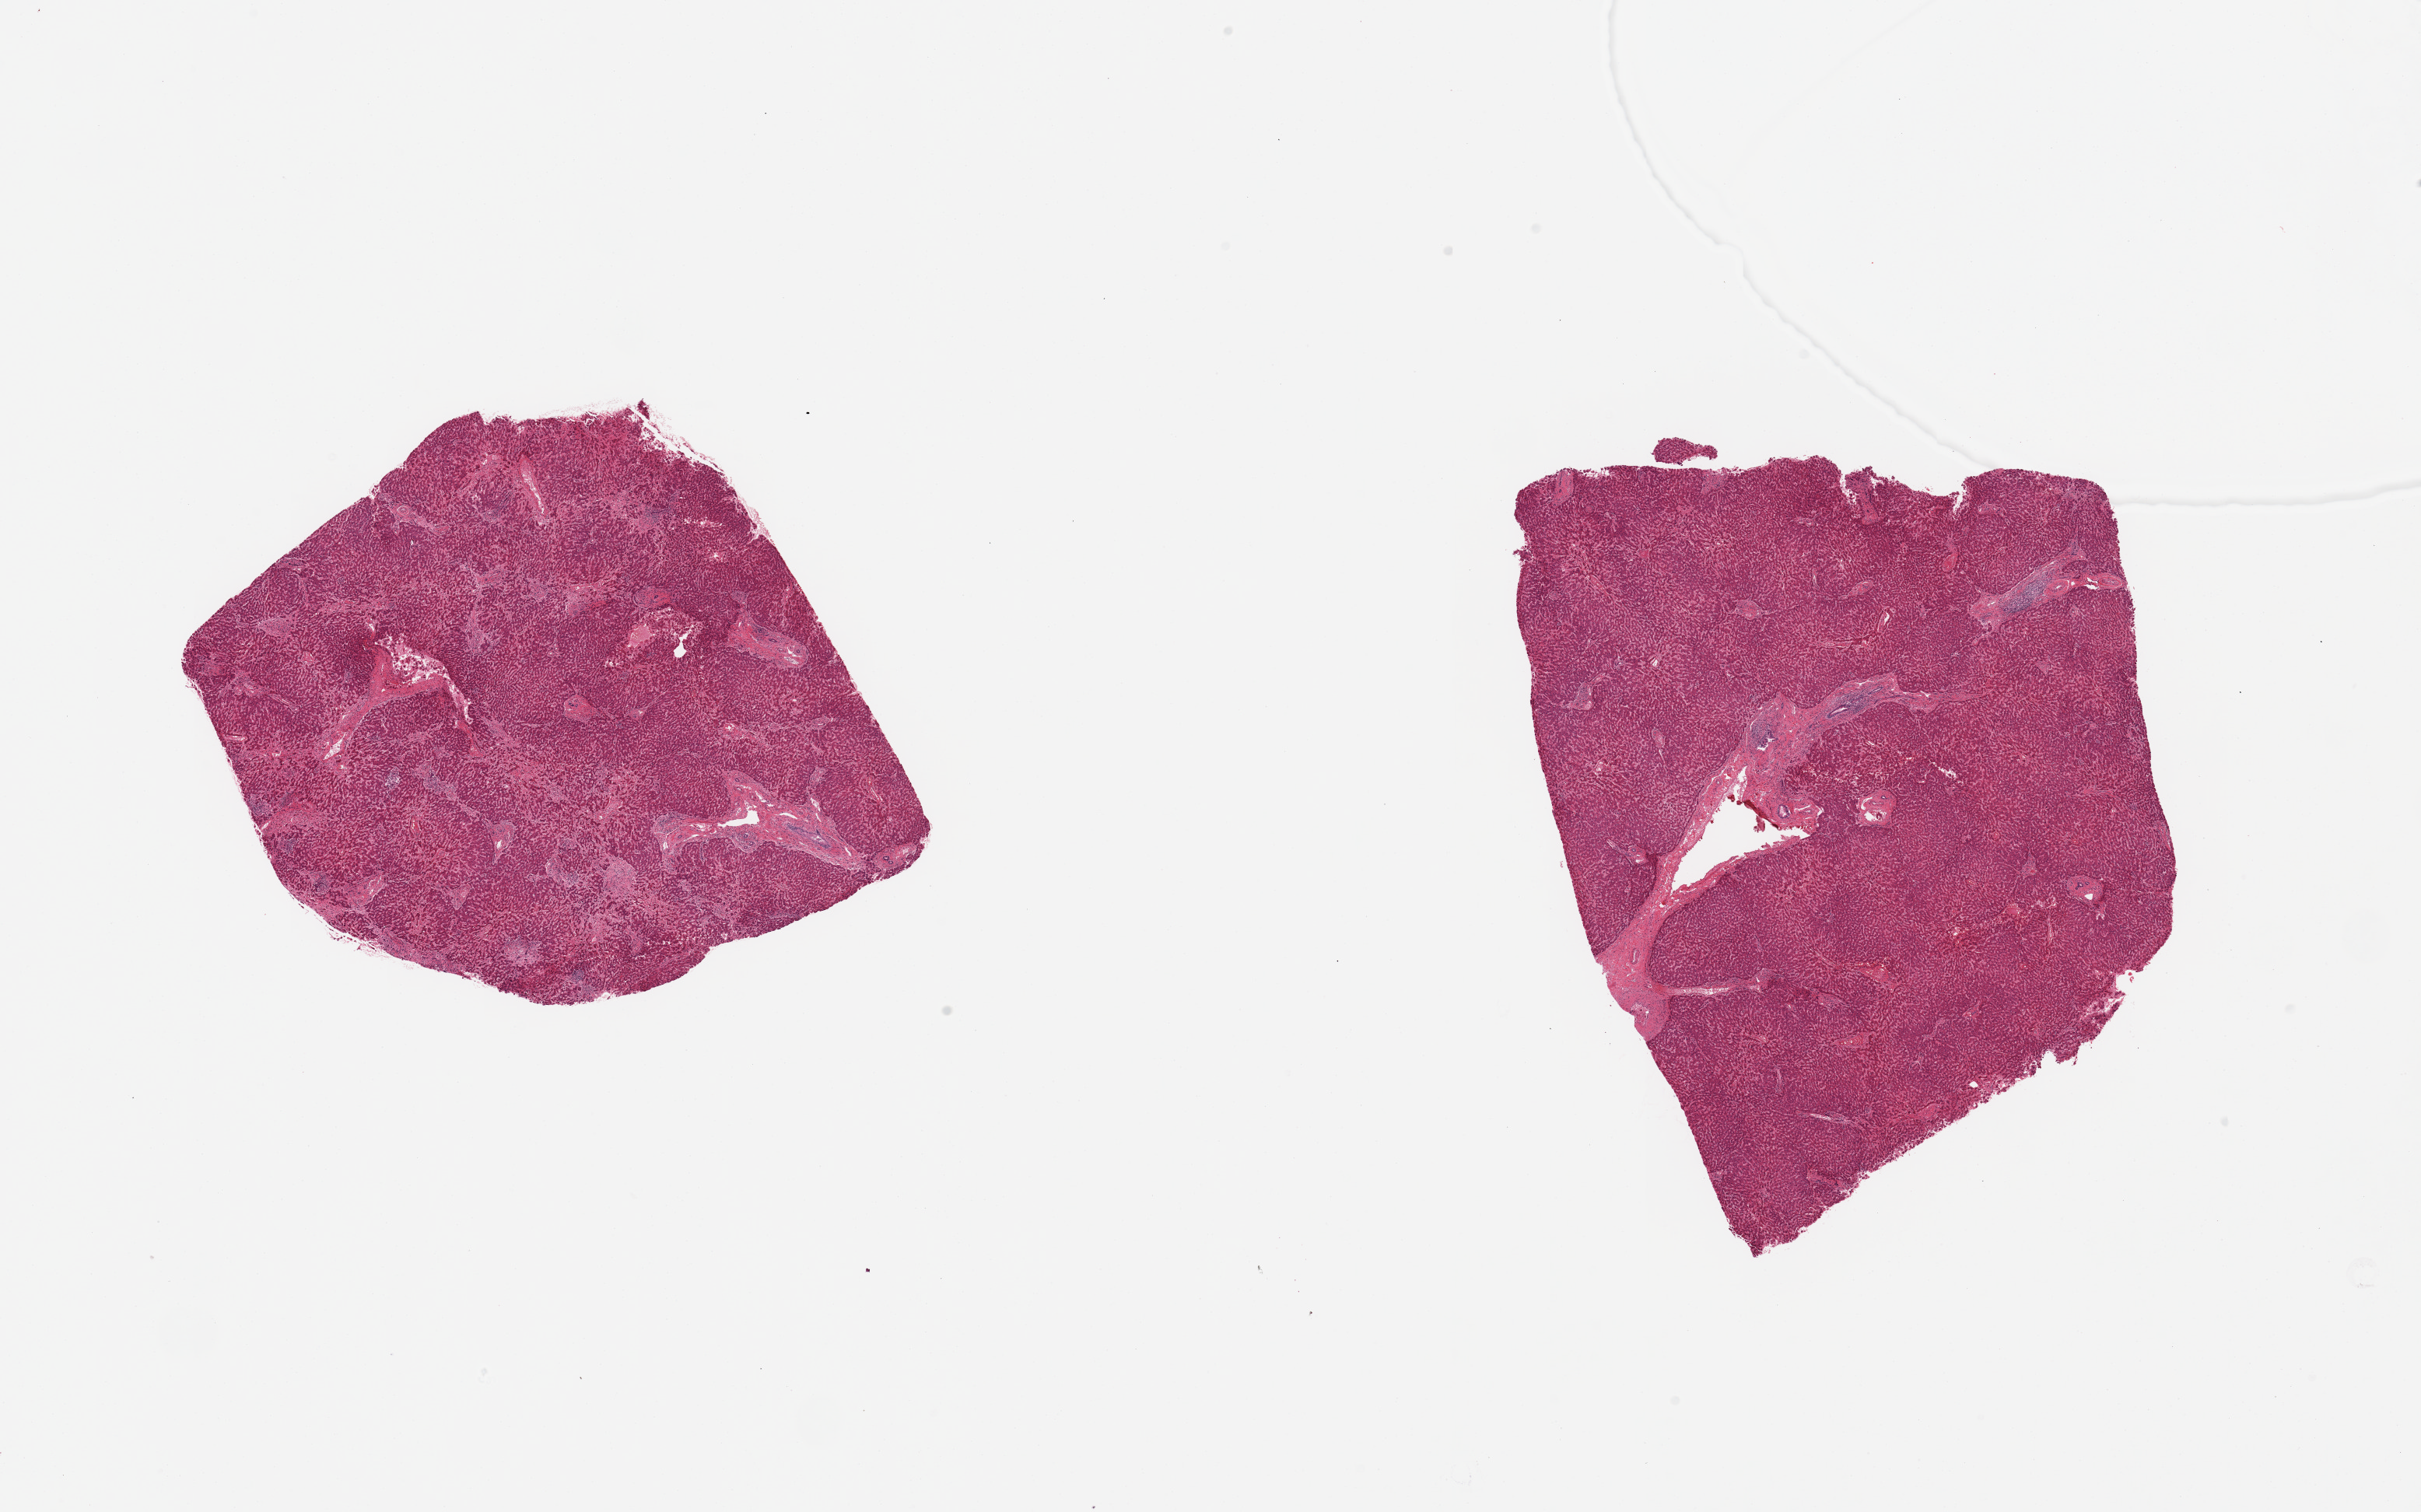
Whole-slide image, H&E stain, brightfield — whole scanned area (about 24.6 x 15.4 mm, acquisition: 20x scan) shown as a low-resolution overview; PAXgene-fixed, paraffin-embedded tissue; target tissue: liver; donor tissue sample.
* reviewer comment on this tissue sample: 2 pieces; periportal and peribiliary chronic inflammation and fibrosis encroaching on liver parenchyma